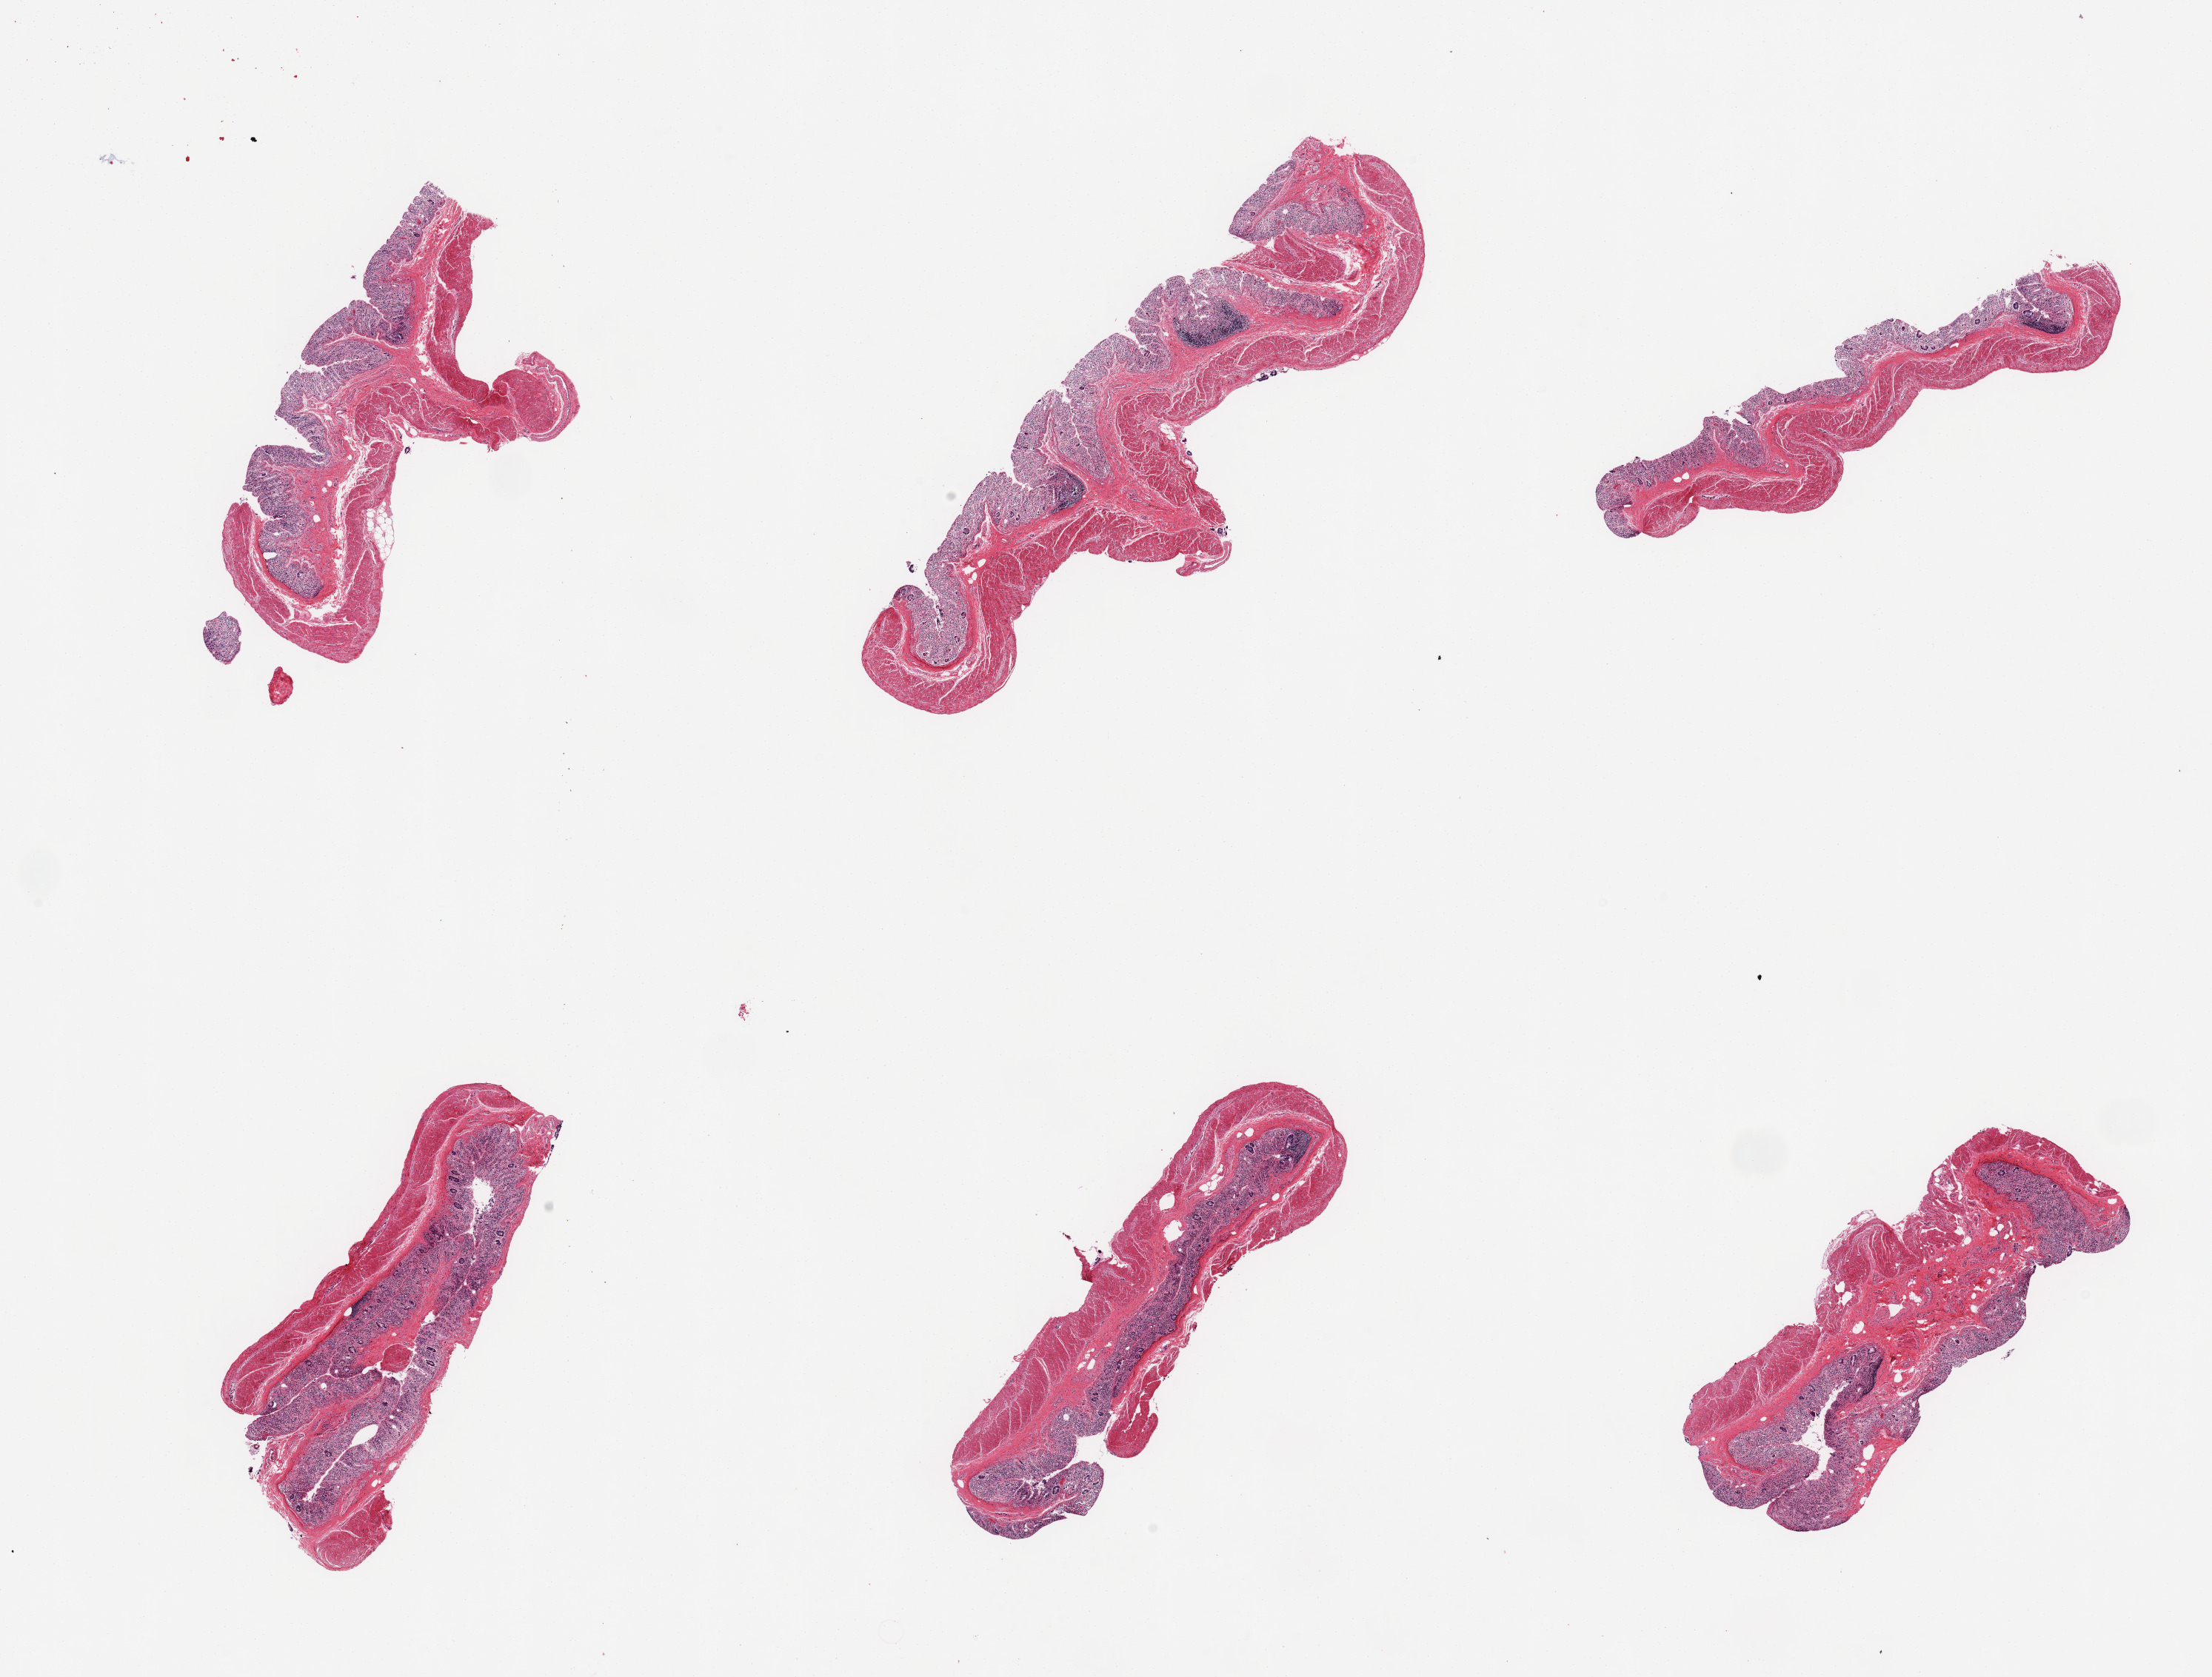
Whole-slide image, H&E stain — whole scanned area (about 23.6 x 17.9 mm) shown as a low-resolution overview. PAXgene-fixed paraffin-embedded (PFPE) section. Section of transverse colon (target tissue). Donor tissue sample. Donor sex: male.
Review note (as recorded): 6 pieces, mucusa up to ~0.2mm, completely autolyzed/sloughing.